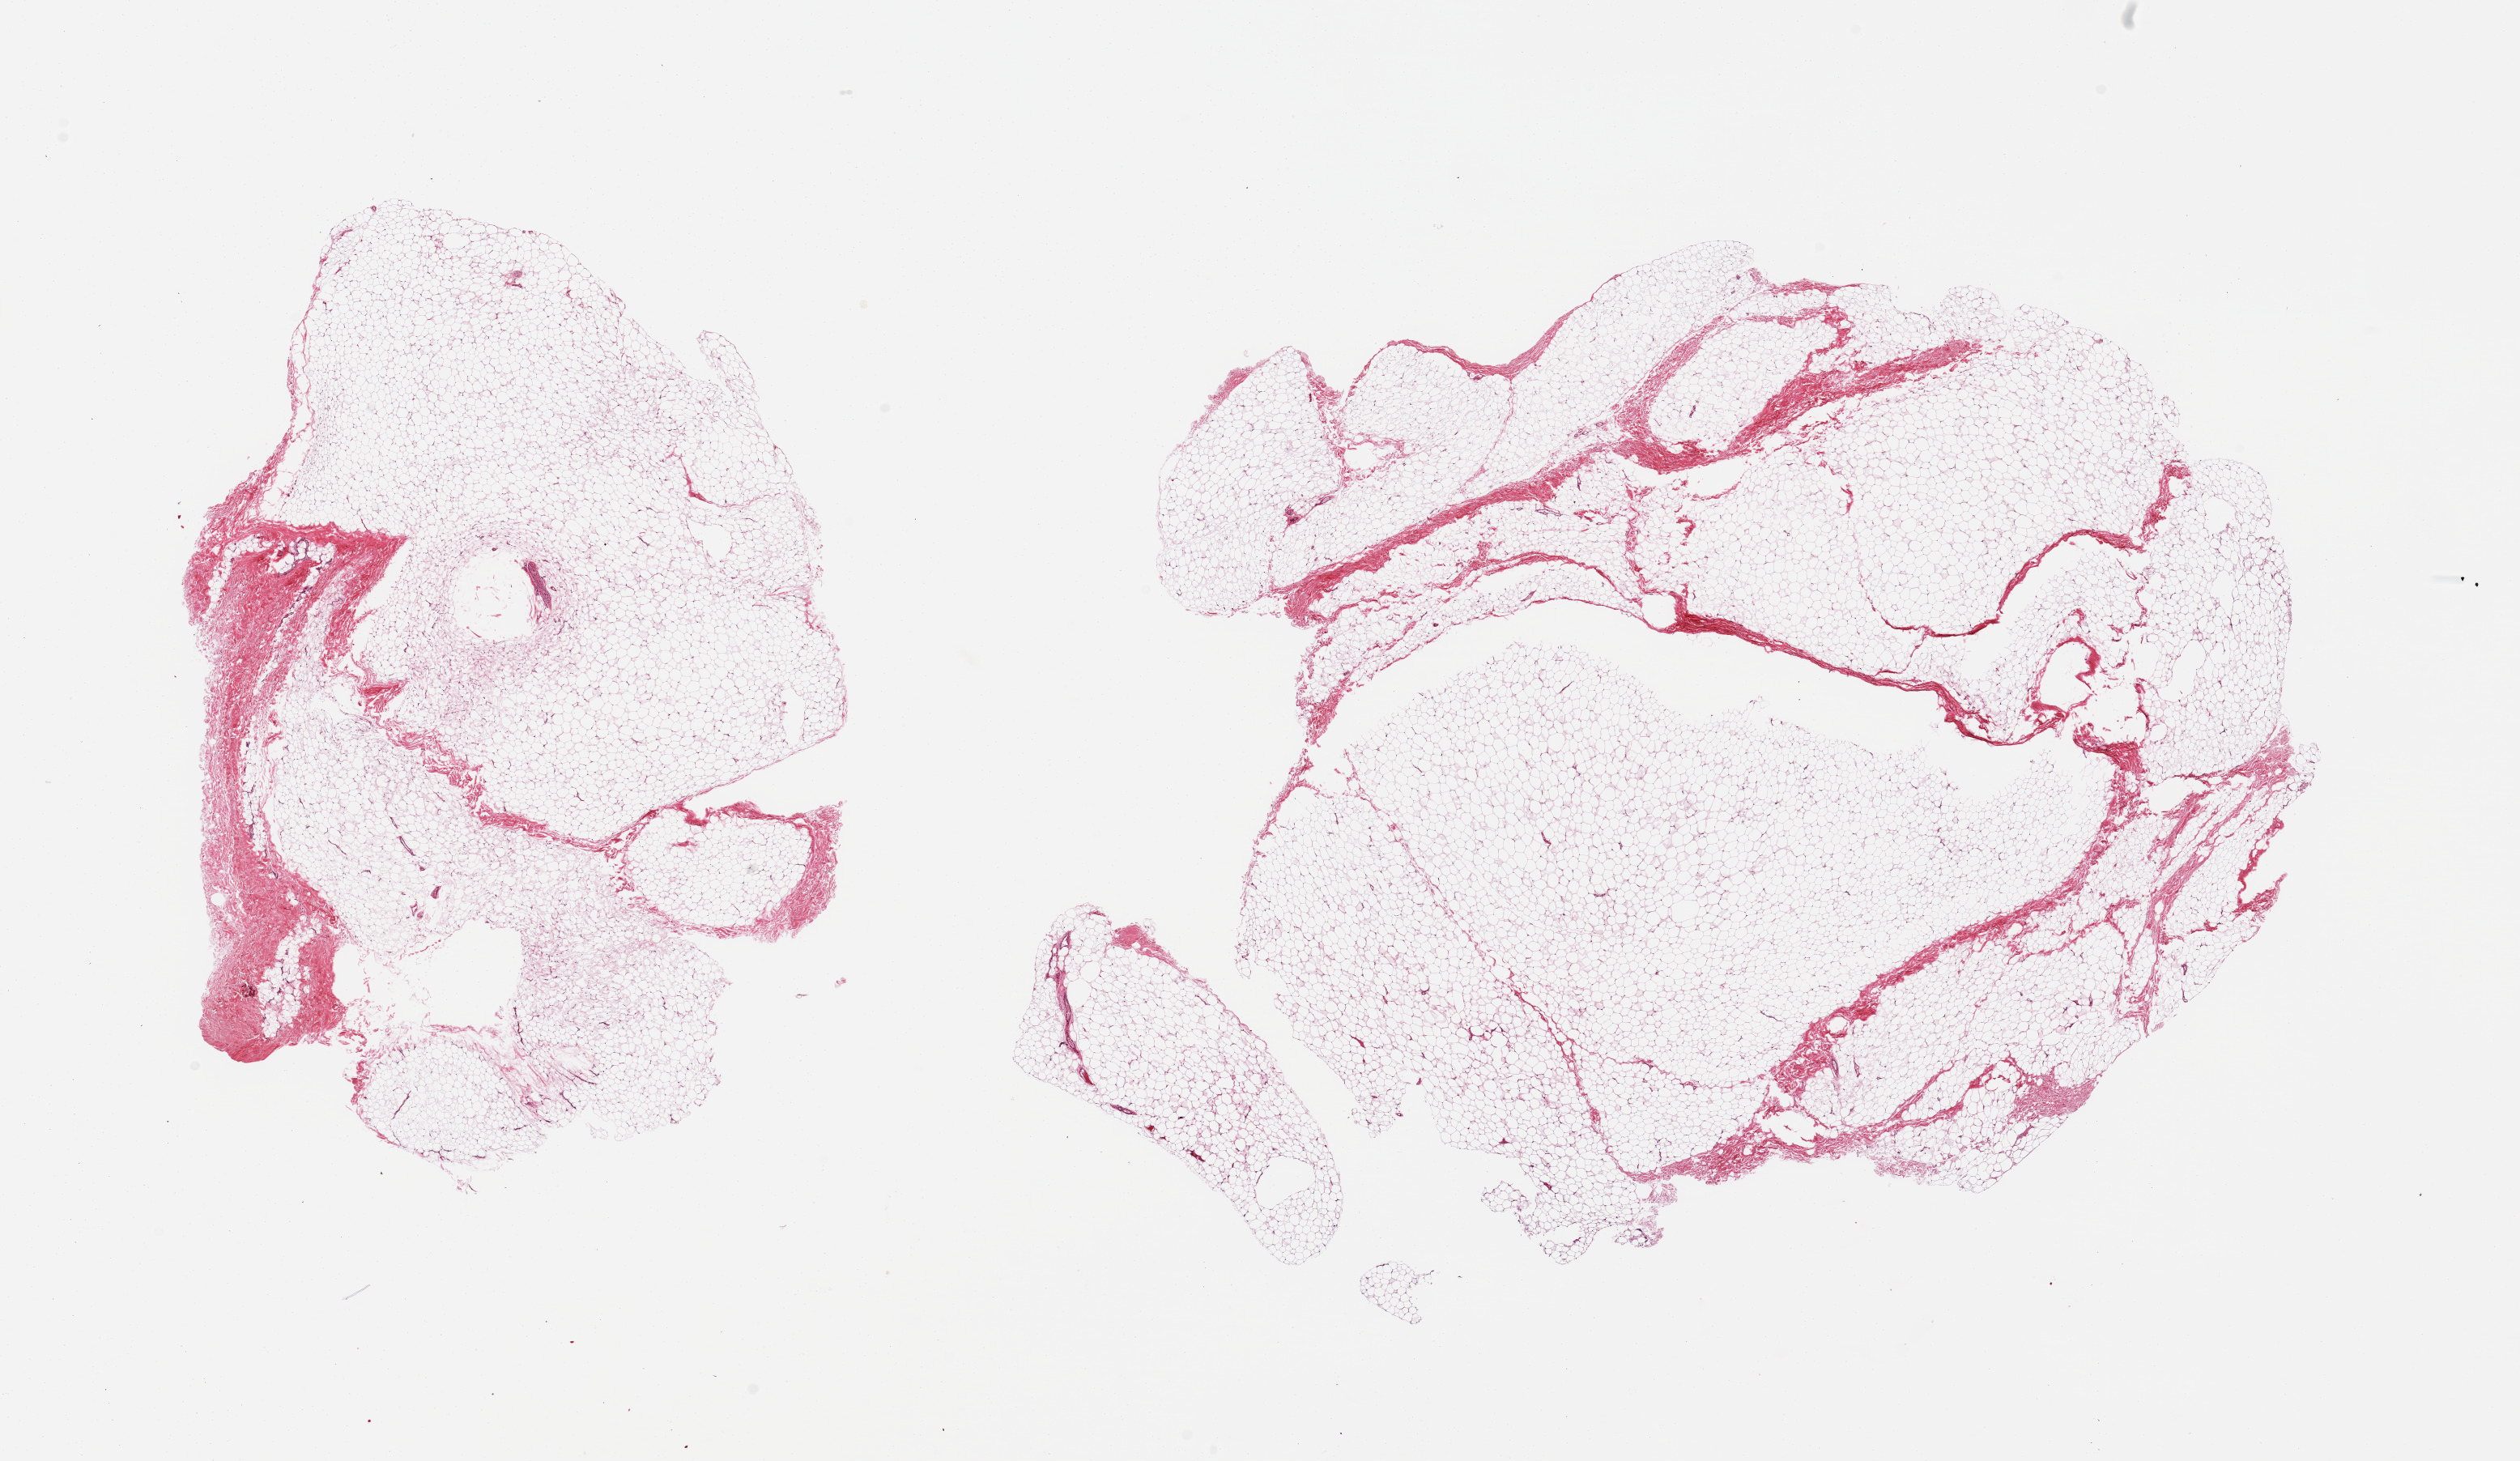
H&E whole-slide image — shown as a low-resolution overview of the whole scanned area (about 24.6 x 14.3 mm), PAXgene-fixed, paraffin-embedded tissue, sampled site (target tissue): breast, tissue donor sample. Donor: male.
Pathologist's review note for this sample: 2 pieces; fat with minor component of stroma (~10%).